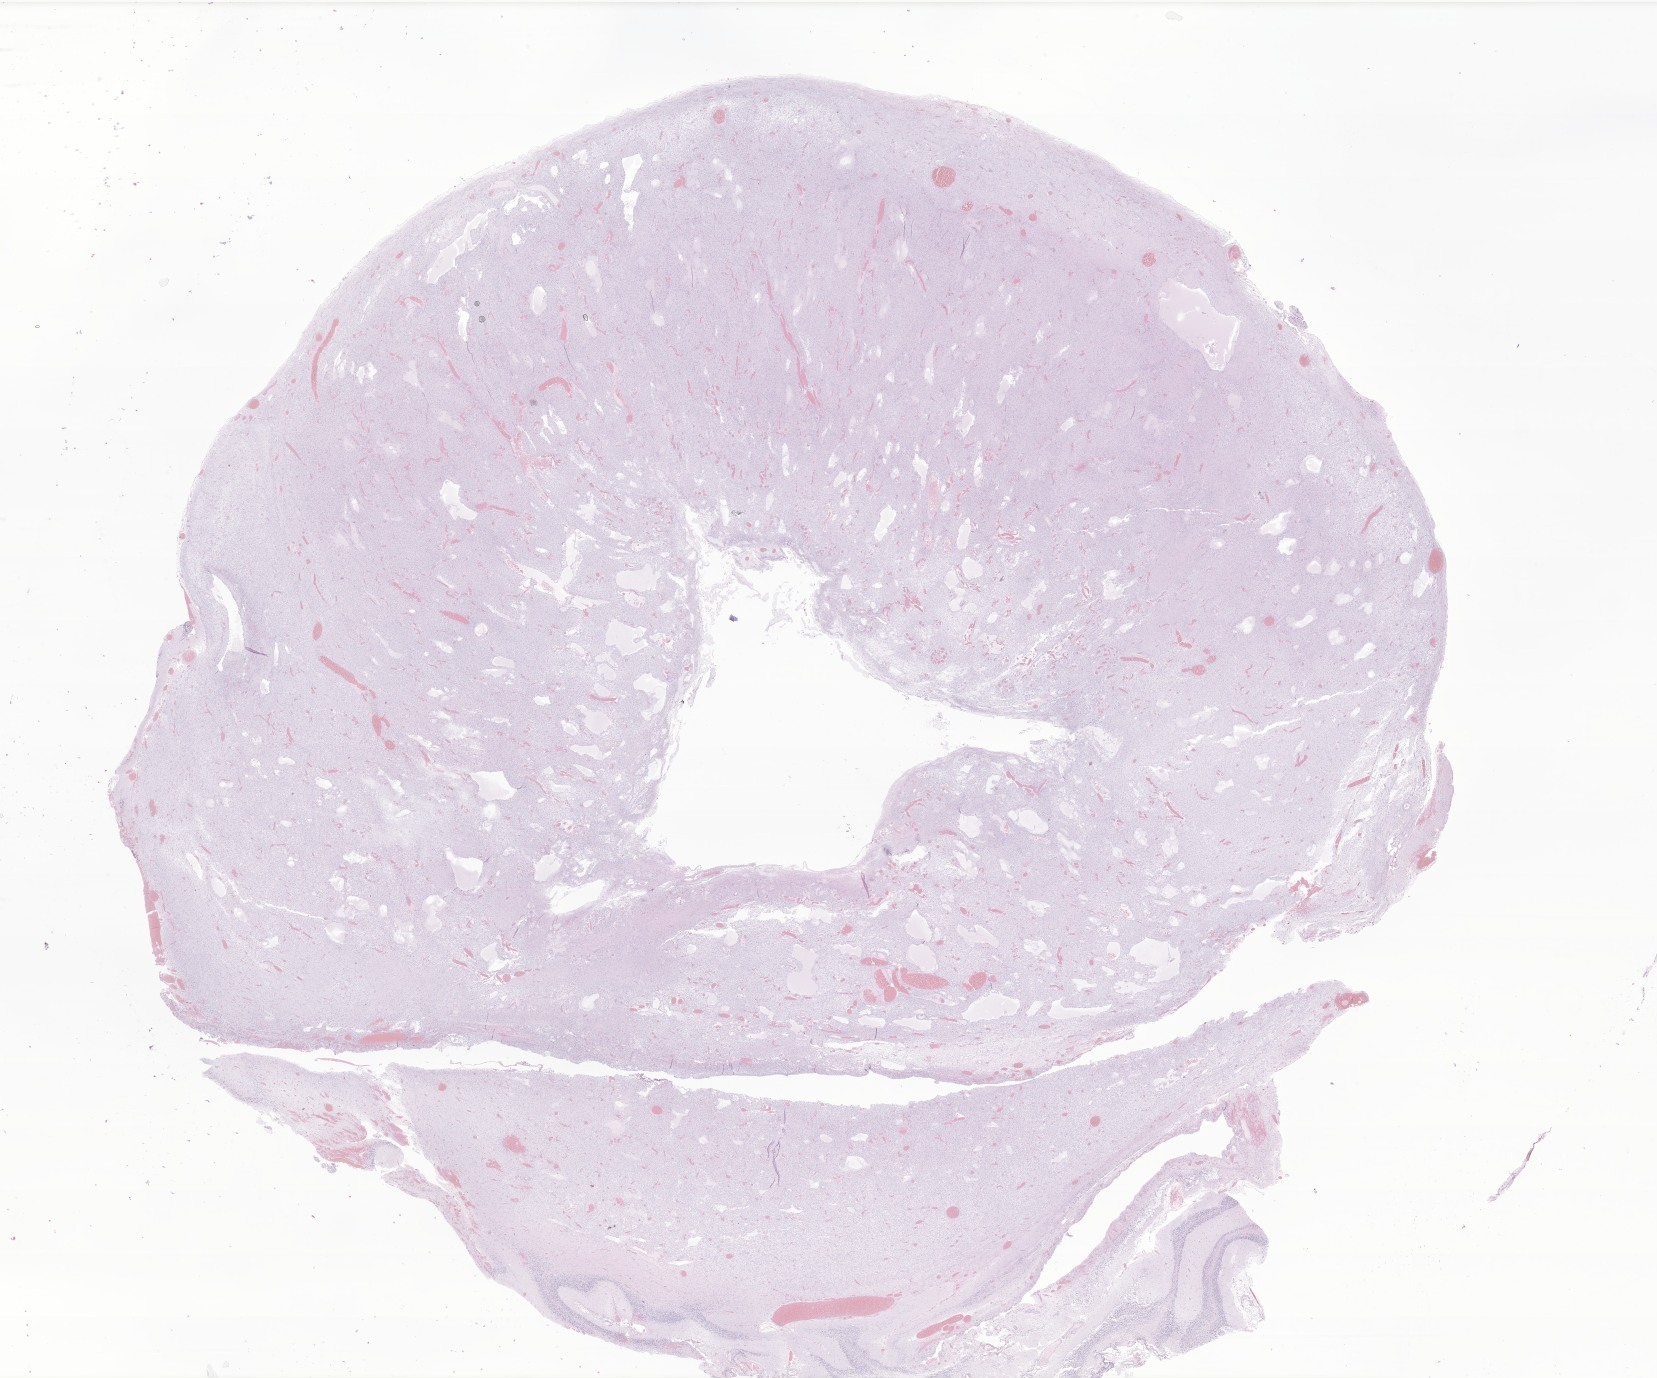
Digitized haematoxylin and eosin-stained section of tumor tissue from the cerebellum, a low-resolution overview of the entire scanned area, about 27.9 x 23.2 mm, FFPE section. Patient: female, age 132 months (11 years).
Recorded diagnosis: Astrocytoma, NOS.